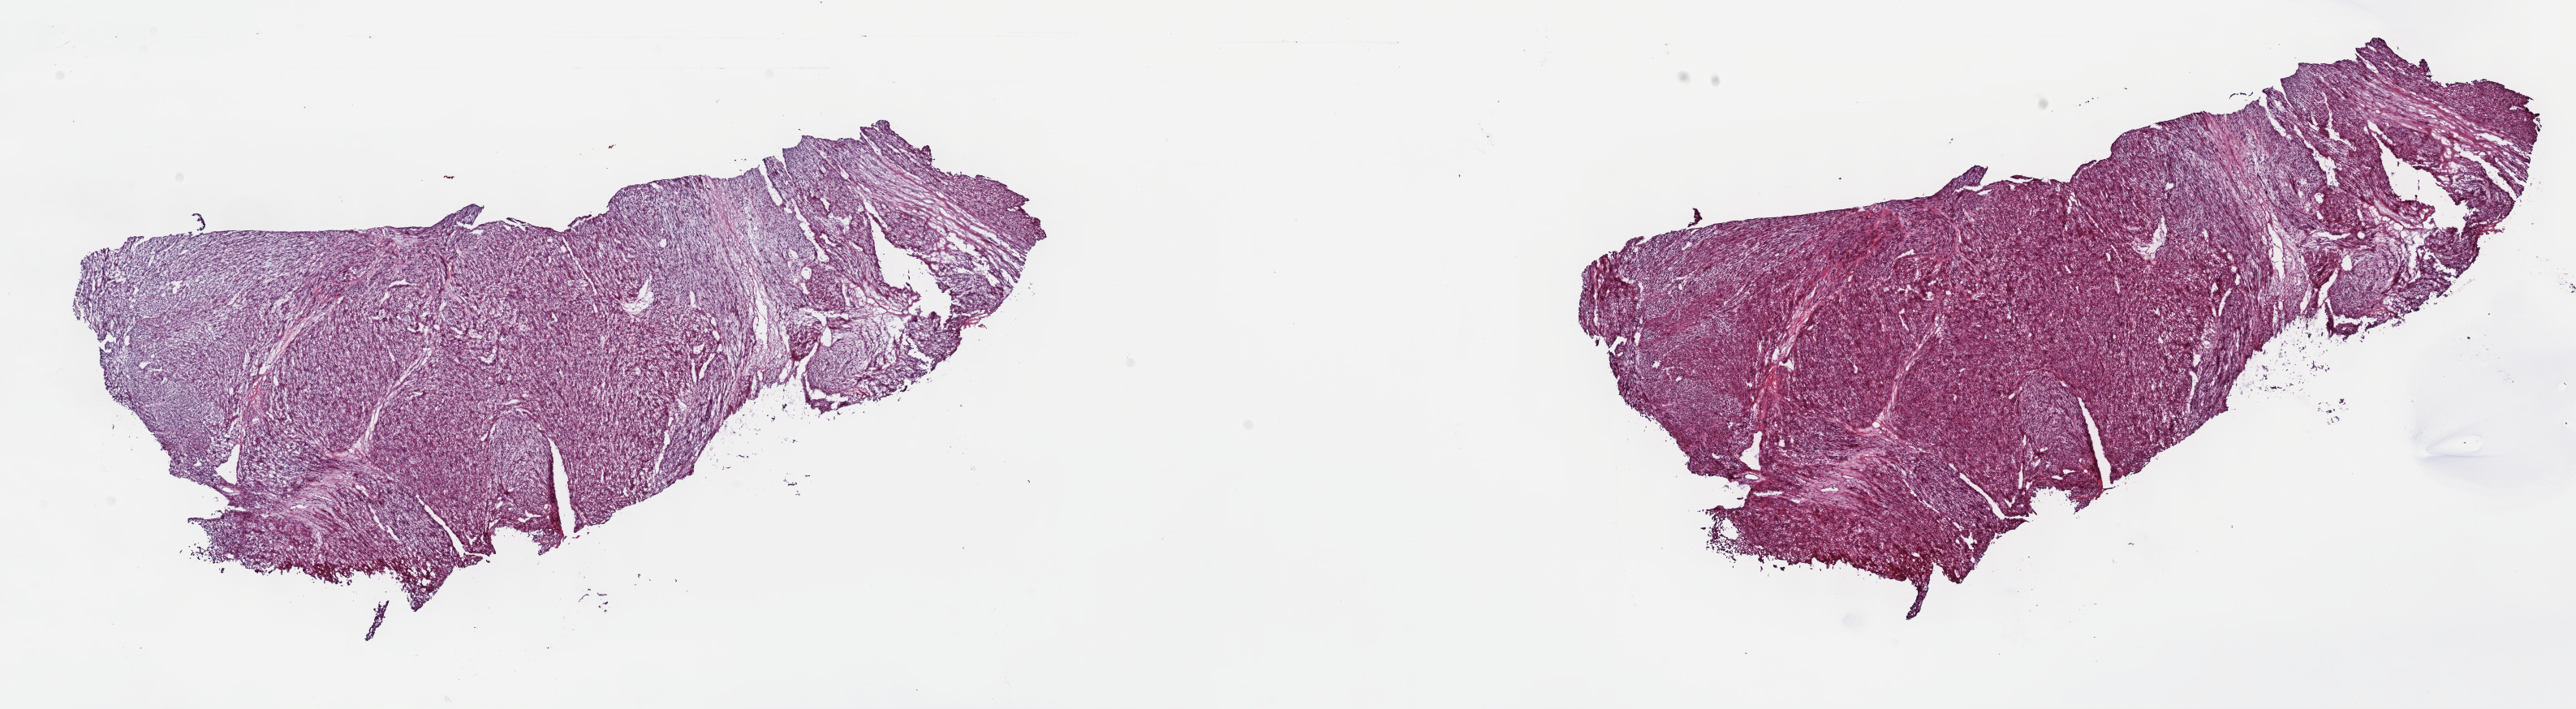
Whole-slide histology image, Hematoxylin and eosin (H&E) stained, whole scanned area (about 25.7 x 7.1 mm) shown as a low-resolution overview, frozen section from the top of the tissue portion, connective, subcutaneous and other soft tissues, primary tumour sample. Female patient; age at initial diagnosis 38 years. Slide review estimates, as recorded: tumour cells 100%, tumour nuclei 80%, normal cells 0%, stromal cells 0%, necrosis 0%. Inflammatory infiltration, as recorded: lymphocyte infiltration 1%, monocyte infiltration 0%, neutrophil infiltration 0%.
Diagnosis: Leiomyosarcoma, NOS.